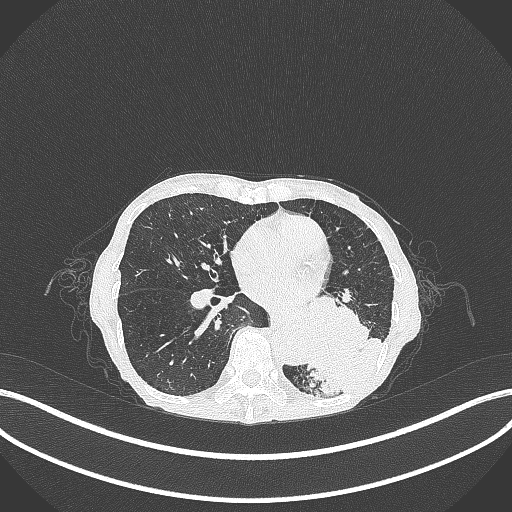
Chest CT, one axial slice; position 119 of 347 along the scan axis; reconstruction kernel B70f; 120 kVp; lung window (W 1500 / L -600 HU); 1 mm slice thickness; 512 × 512 image matrix, field of view 400 × 400 mm. Female patient, age 70 years. Case-level facts recorded for this patient, not image findings: clinical TNM (as recorded): T3 N0 M0; histopathological grade: G3.
Outlined on this slice (rectangle marked by the reading radiologist):
- lung tumour (recorded histology: small cell carcinoma): box from (x=292, y=295) to (x=386, y=398) px